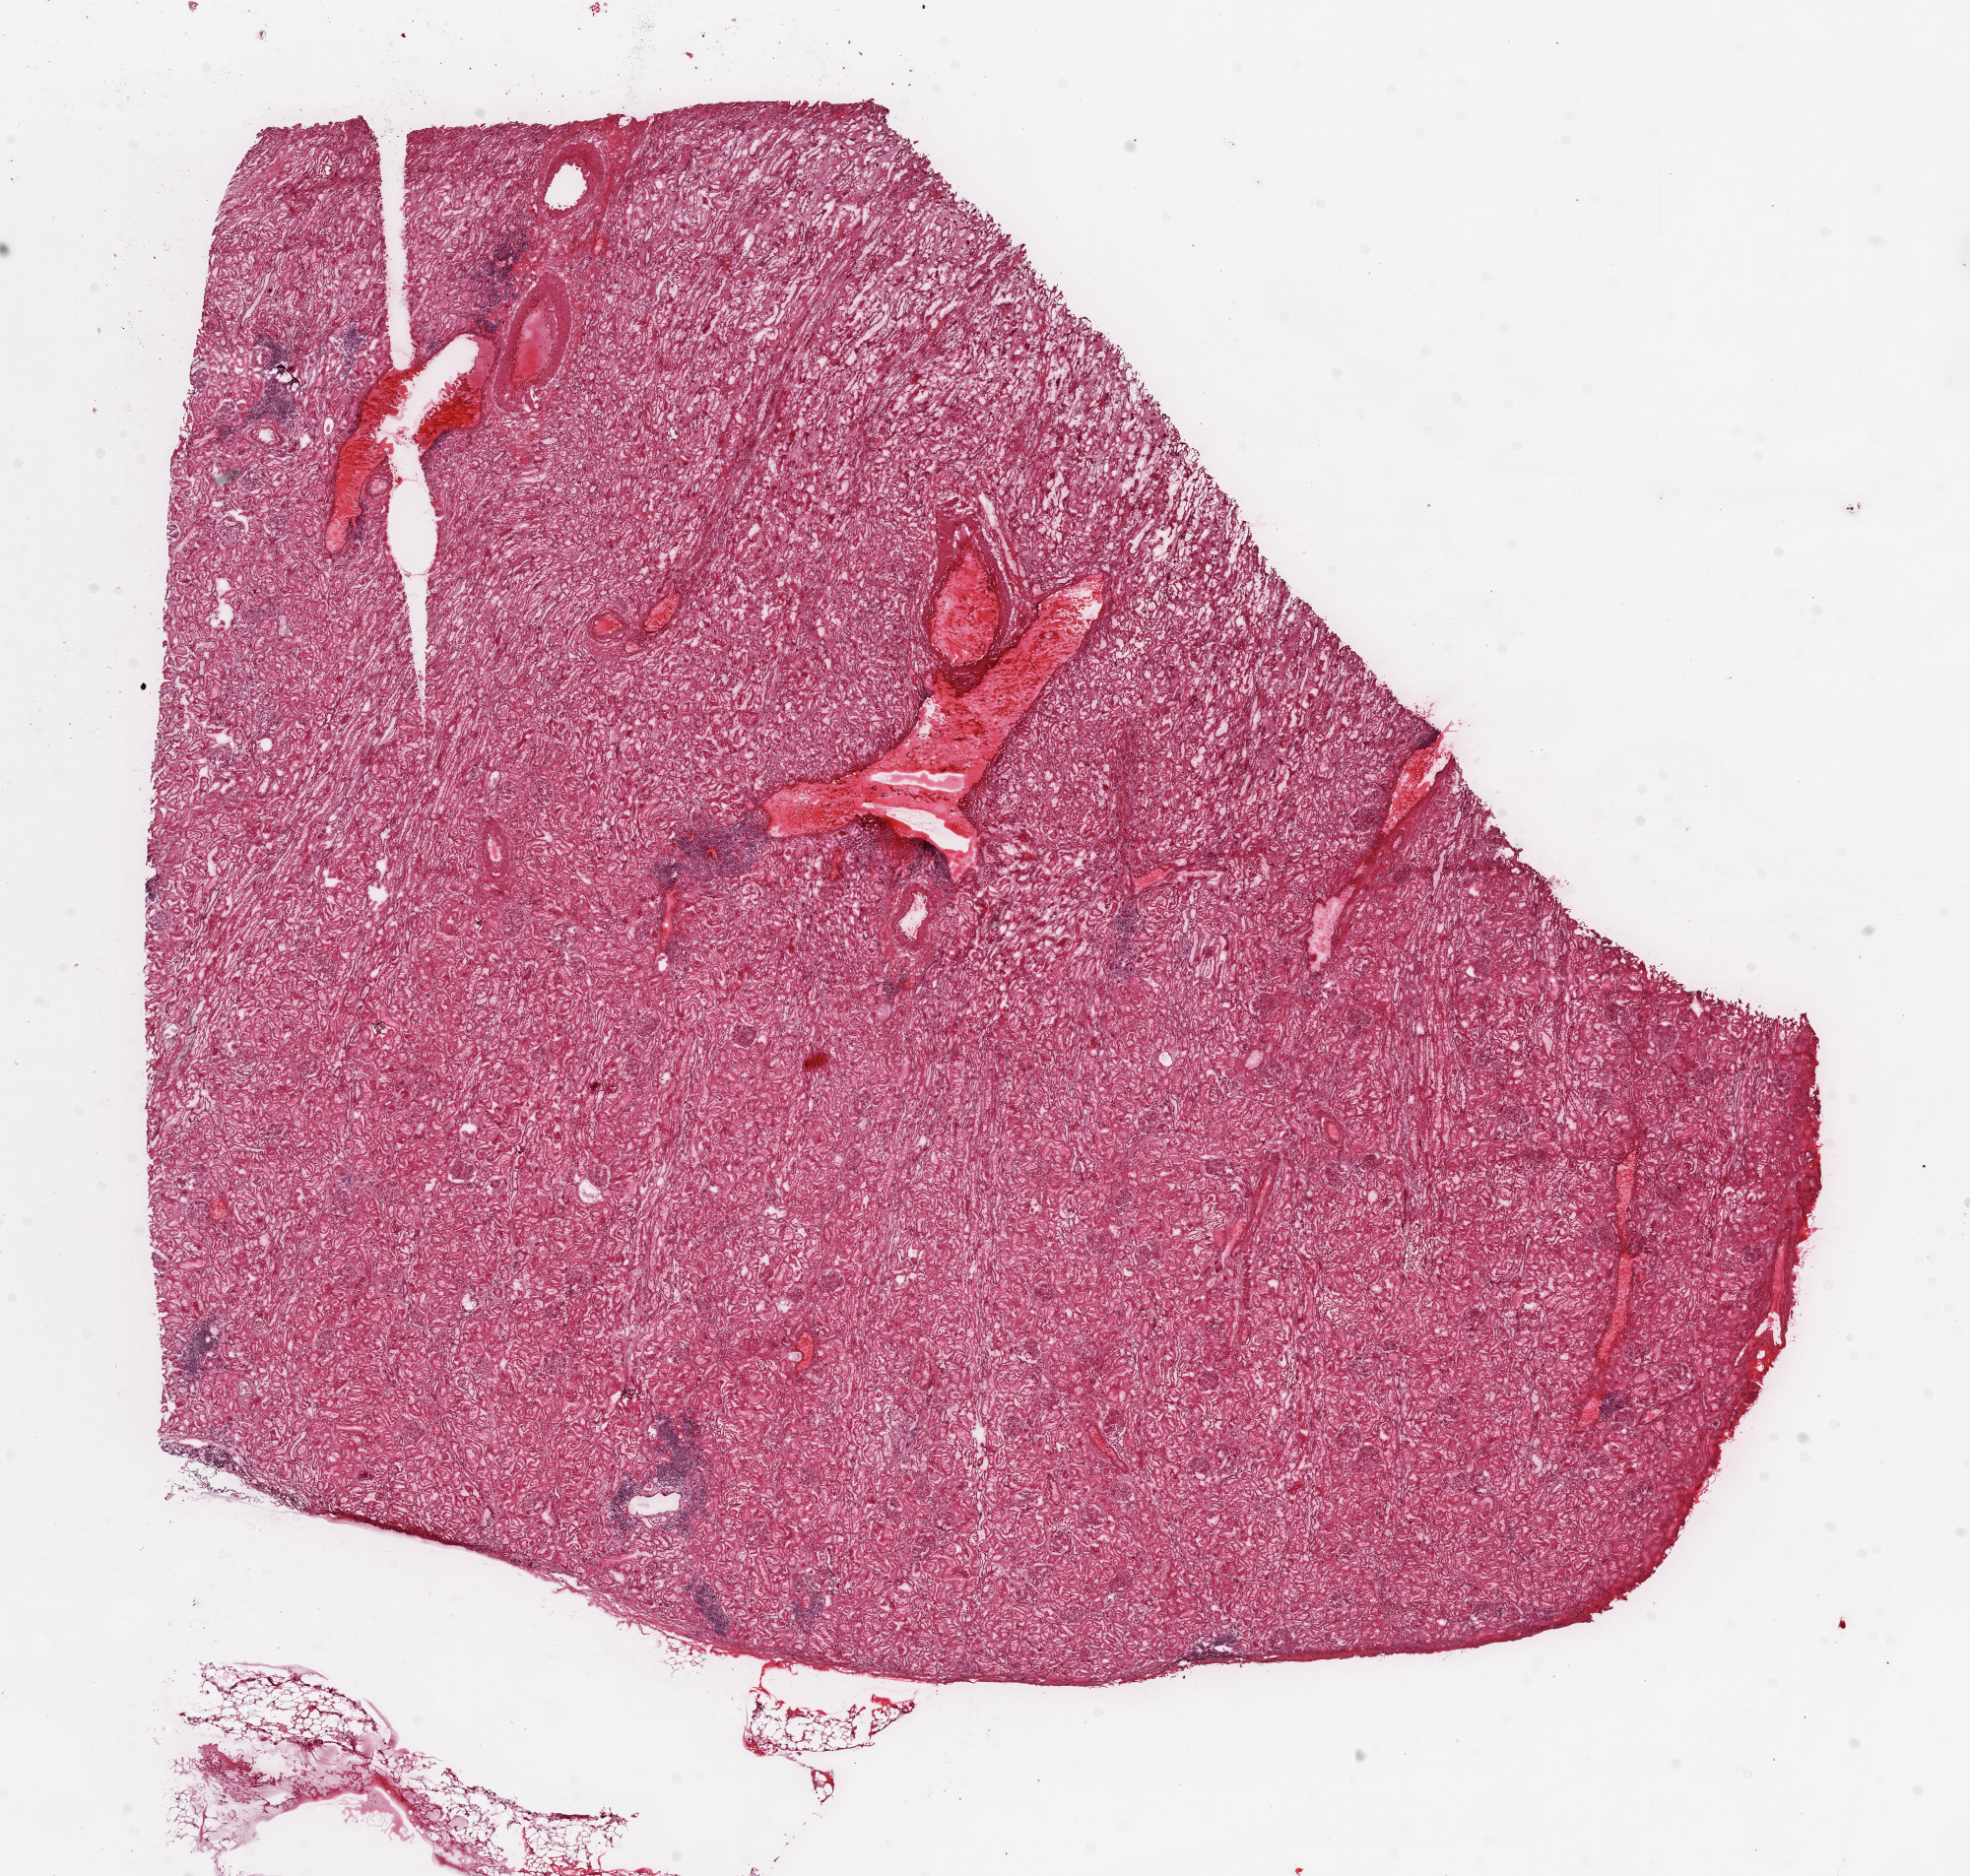
Digitized H&E-stained tissue section (whole slide), low-resolution overview of the scanned area, about 16.0 x 15.3 mm (from a 20x scan), frozen section, sample: solid tissue normal (non-tumour tissue), kidney. Patient: male, age at initial diagnosis 72 years.
This section: solid tissue normal (non-tumour) sample from the same patient. Patient diagnosis: Clear cell adenocarcinoma, NOS.